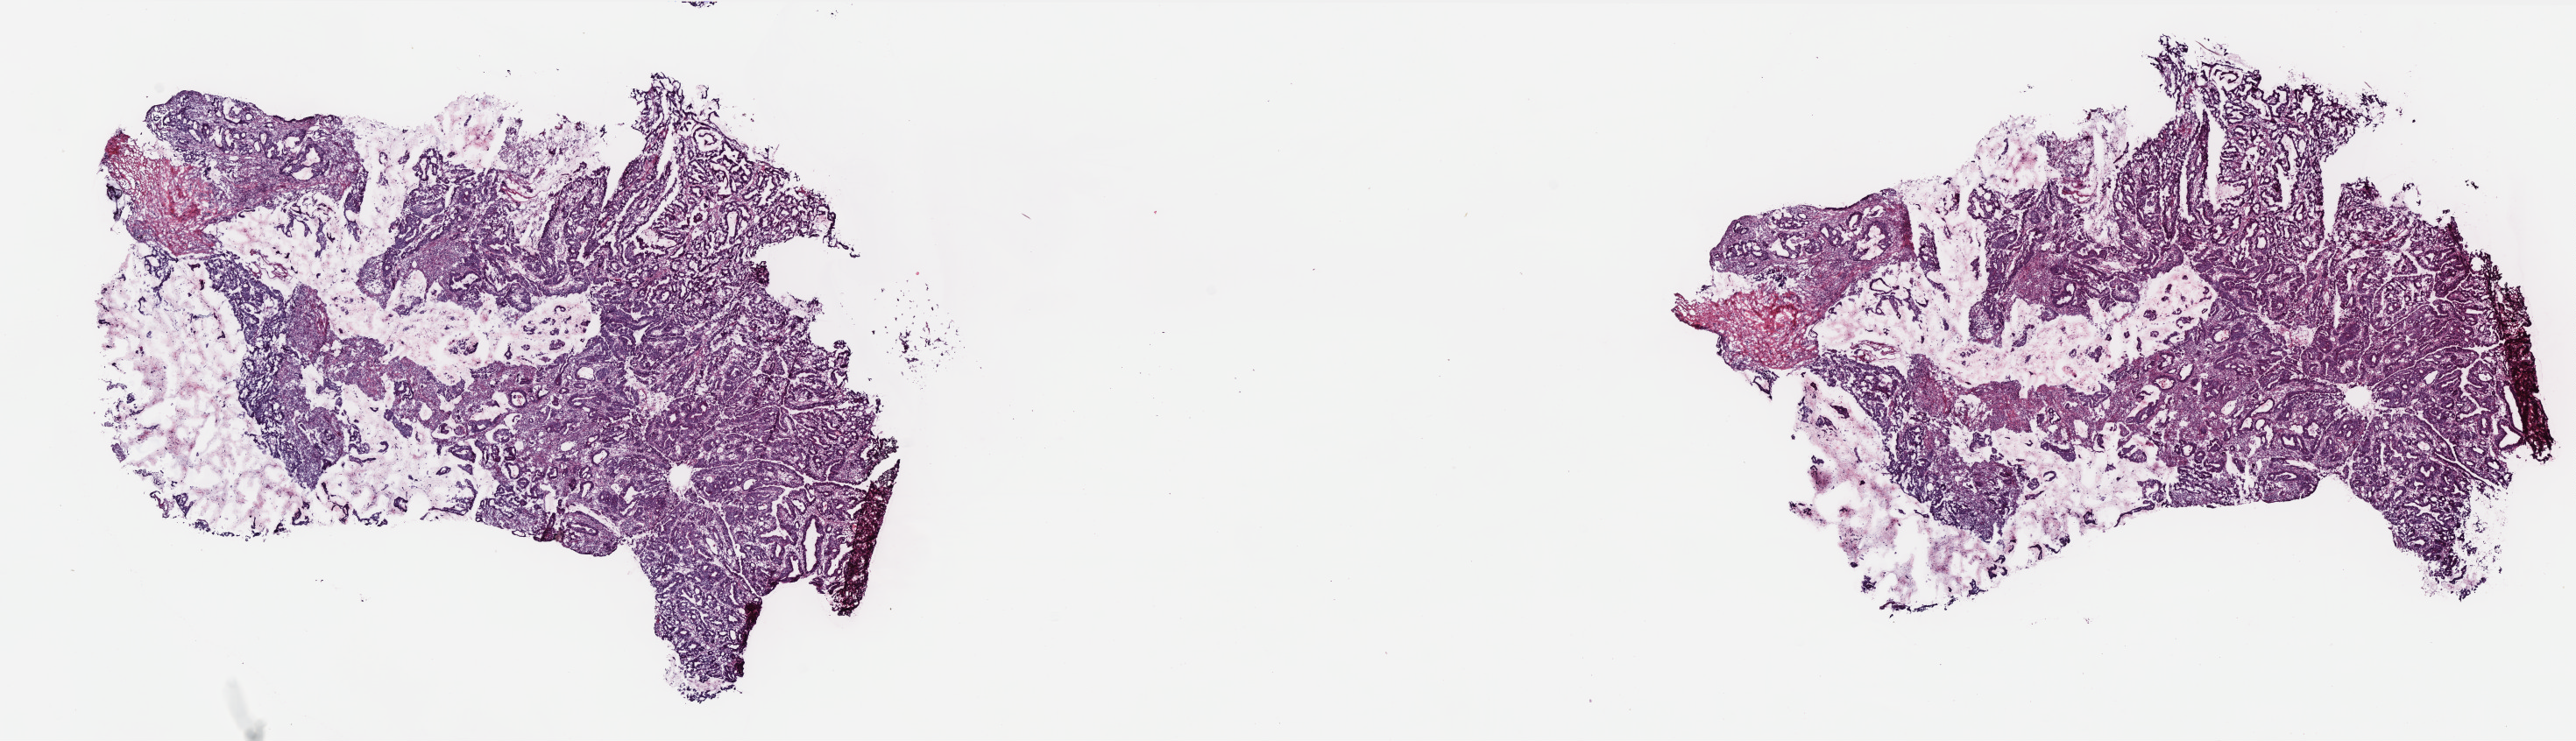
Digitized H&E-stained tissue section (whole slide), whole scanned area (about 23.6 x 6.8 mm, from a 40x scan) shown as a low-resolution overview, frozen section, colon, primary tumour sample. Female, age 47 years at initial diagnosis. Slide review estimates, as recorded: tumour cells 95%, tumour nuclei 75%, normal cells 0%, stromal cells 4%, necrosis 1%. Inflammatory infiltration, as recorded: lymphocyte infiltration 10%, monocyte infiltration 2%, neutrophil infiltration 1%.
AJCC pathologic stage: IIIC (6th edition). Pathologic diagnosis: Mucinous adenocarcinoma (rectosigmoid junction). Lymph nodes positive (case pathology): 12 of 12 examined.